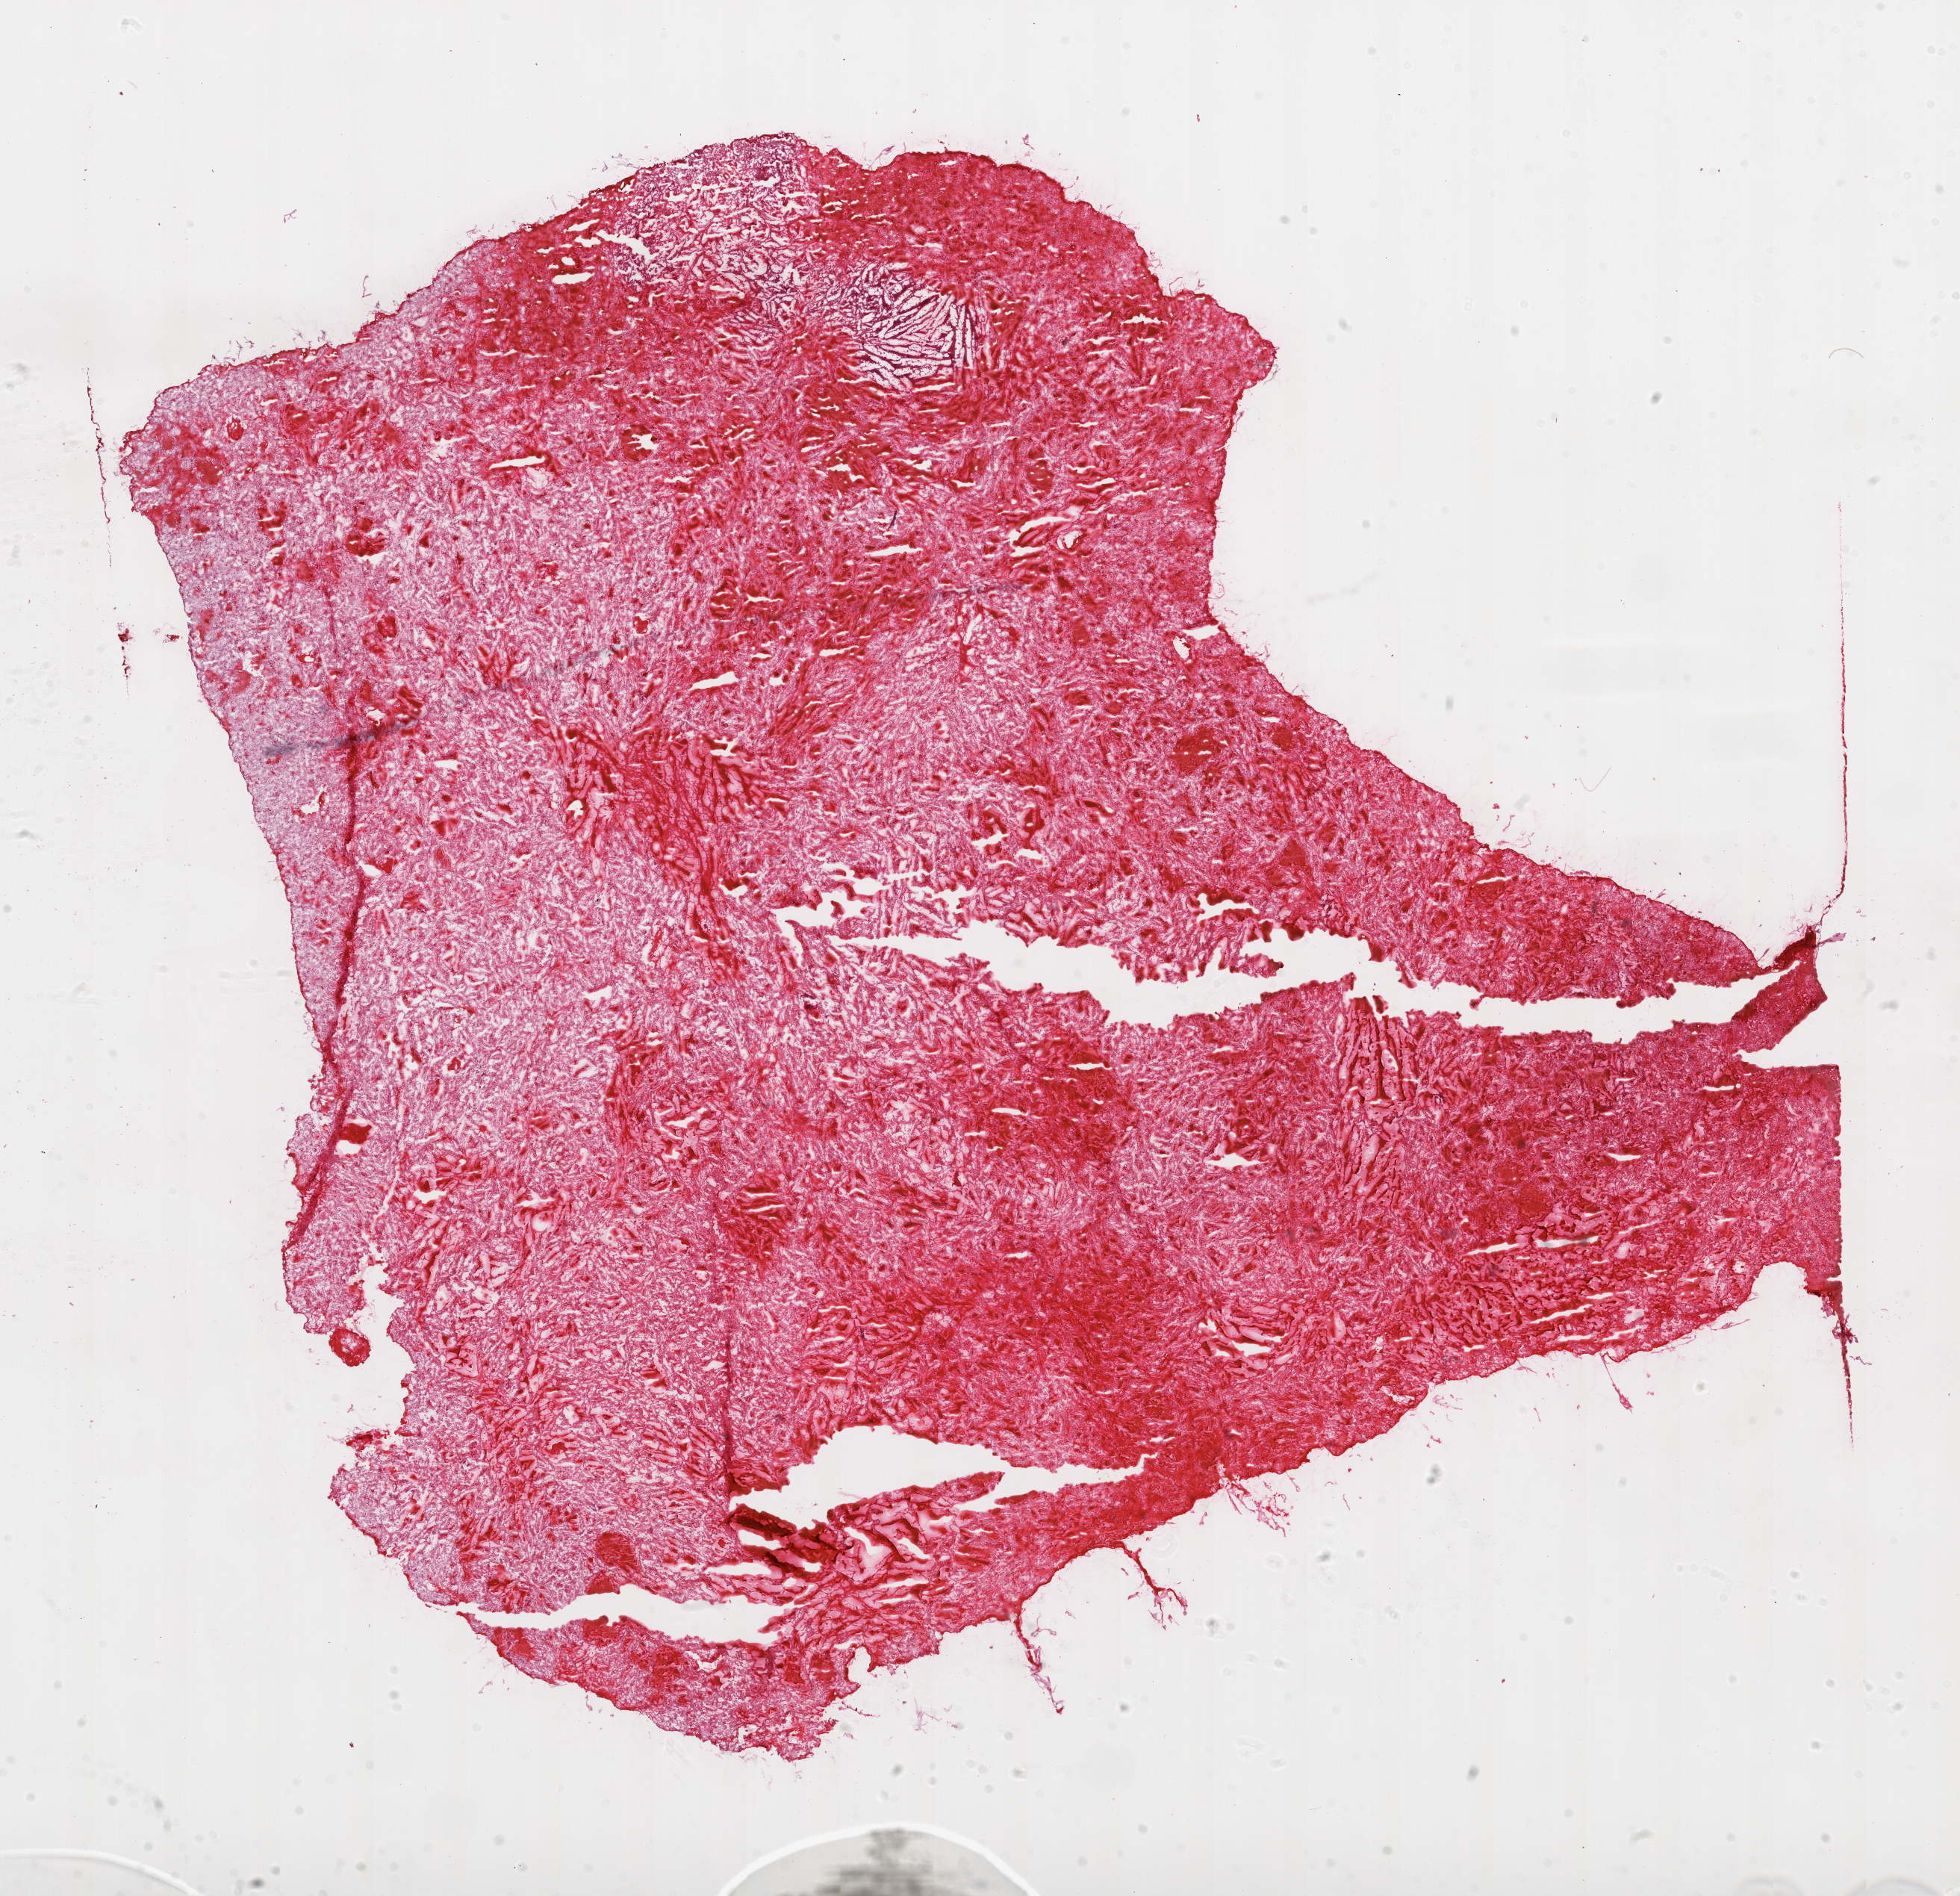
Whole-slide histology image, H&E-stained — a low-resolution overview of the entire scanned area, about 21.1 x 20.4 mm (acquisition: 20x scan), frozen section from the top of the tissue portion, primary tumour sample from the kidney. Male patient; age at initial diagnosis 83 years. Histologic grade: G3 (poorly differentiated). Composition of this section per pathologist review: tumour cells 90%, tumour nuclei 90%, normal cells 0%, stromal cells 10%, necrosis 0%.
- AJCC pathologic stage: IV (6th edition)
- TNM: T1b NX M1
- diagnosis: Clear cell adenocarcinoma, NOS